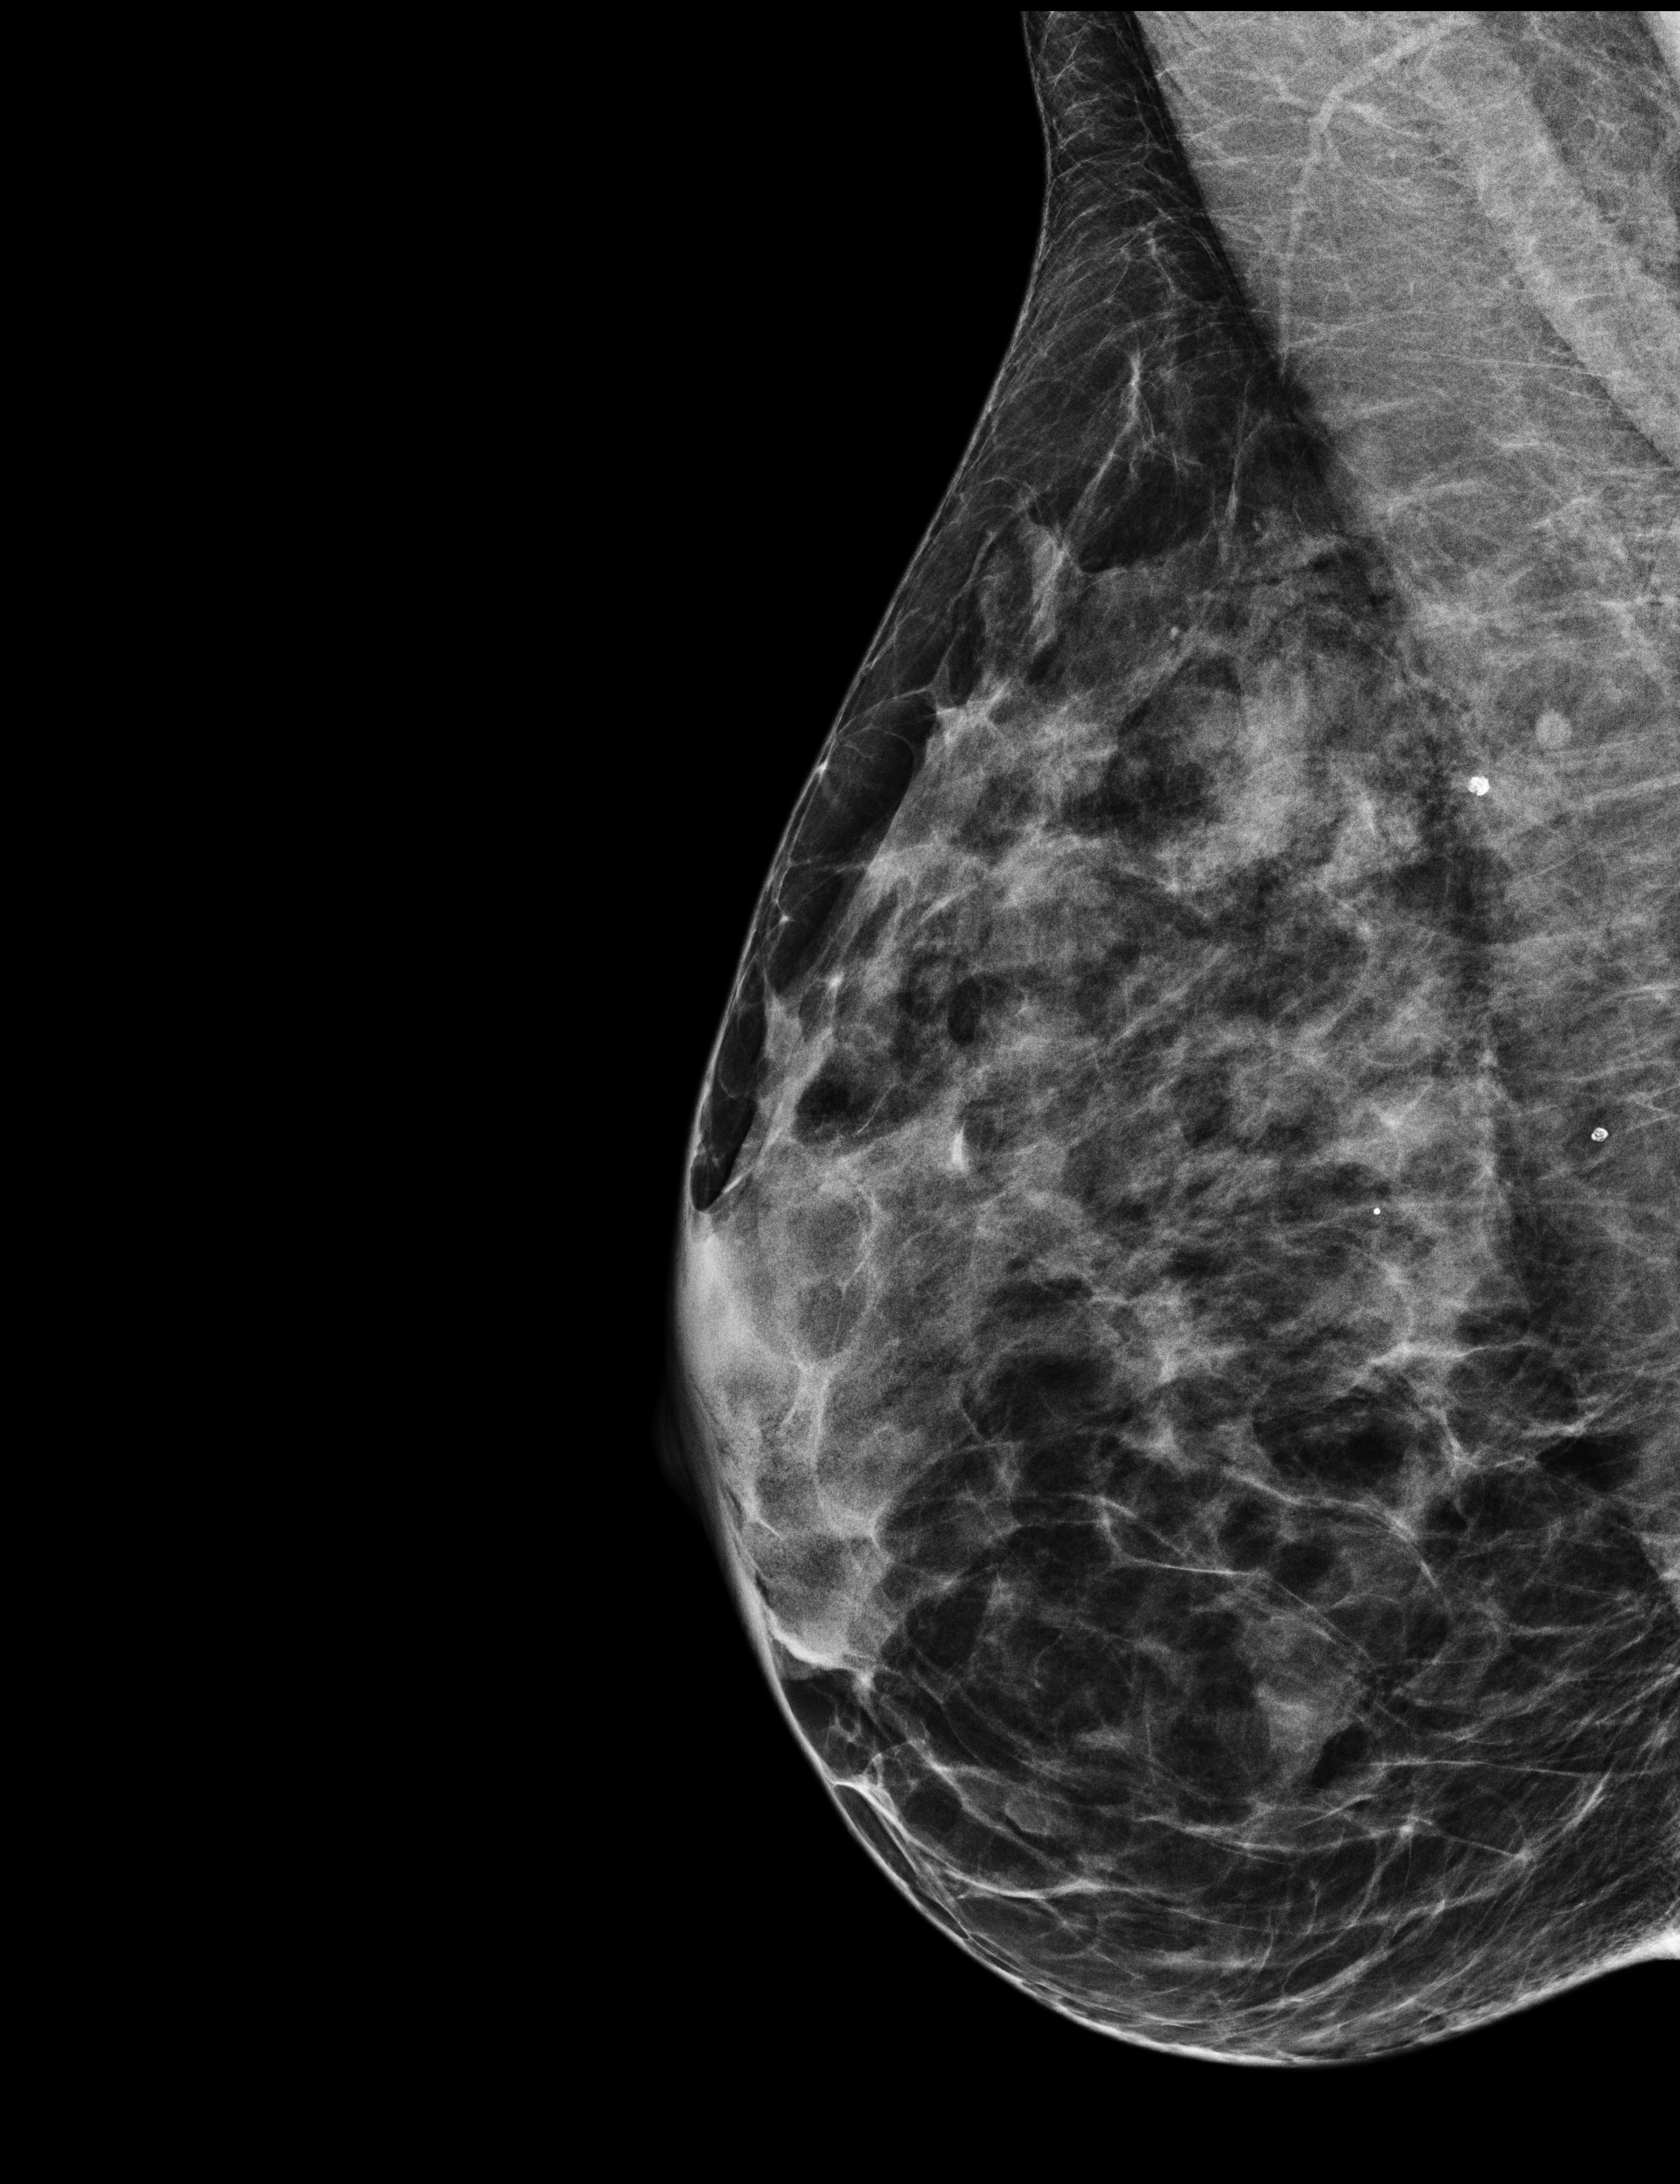
Screening examination, compressed breast thickness 44 mm, system: Selenia Dimensions. Female patient, age 55 years.
Image type: full-field digital mammogram. Breast: right. Projection: mediolateral oblique (MLO) view.